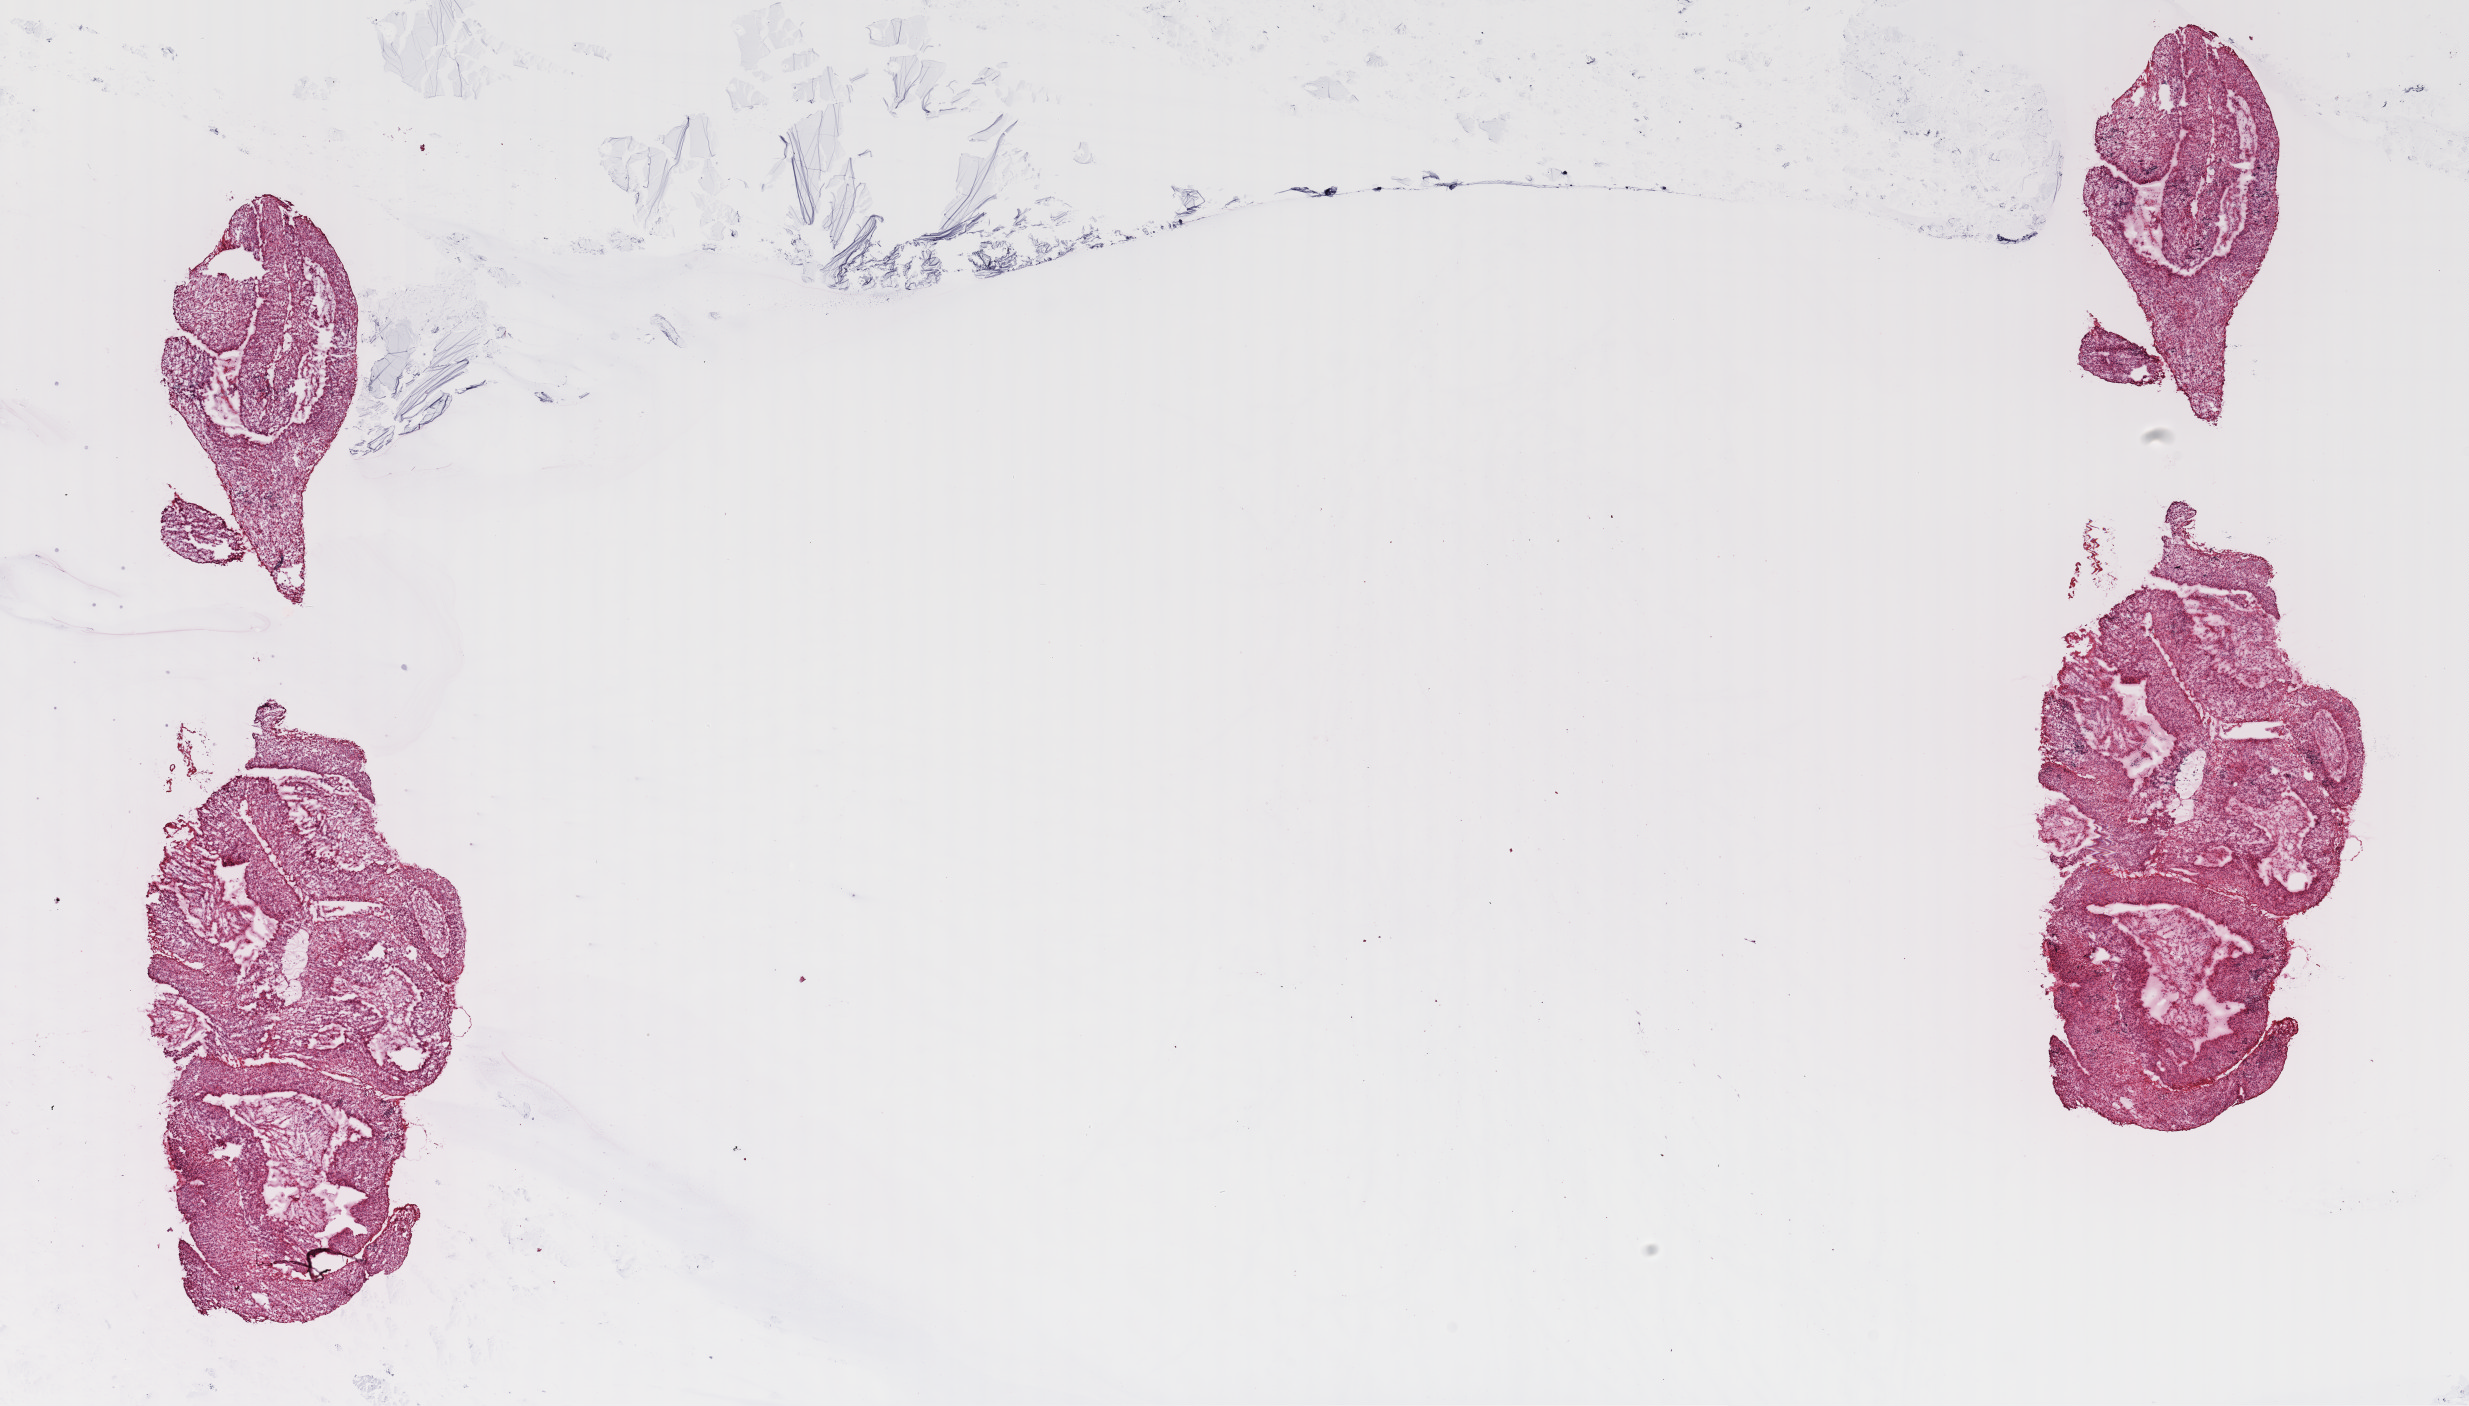
Digitized H&E-stained tissue section (whole slide), low-resolution overview of the scanned area, about 19.5 x 11.1 mm (slide scanned at 40x). Frozen section from the top of the tissue portion. Sample: primary tumour, lung. Patient: male, age at initial diagnosis 59 years. Slide review estimates, as recorded: tumour cells 100%, tumour nuclei 90%, normal cells 0%, stromal cells 0%, necrosis 0%. Infiltration values recorded for this section: lymphocyte infiltration 0%, monocyte infiltration 0%, neutrophil infiltration 0%.
AJCC pathologic stage: IIIA (6th edition). Pathologic diagnosis: Basaloid squamous cell carcinoma (lower lobe, lung). Laterality: right.